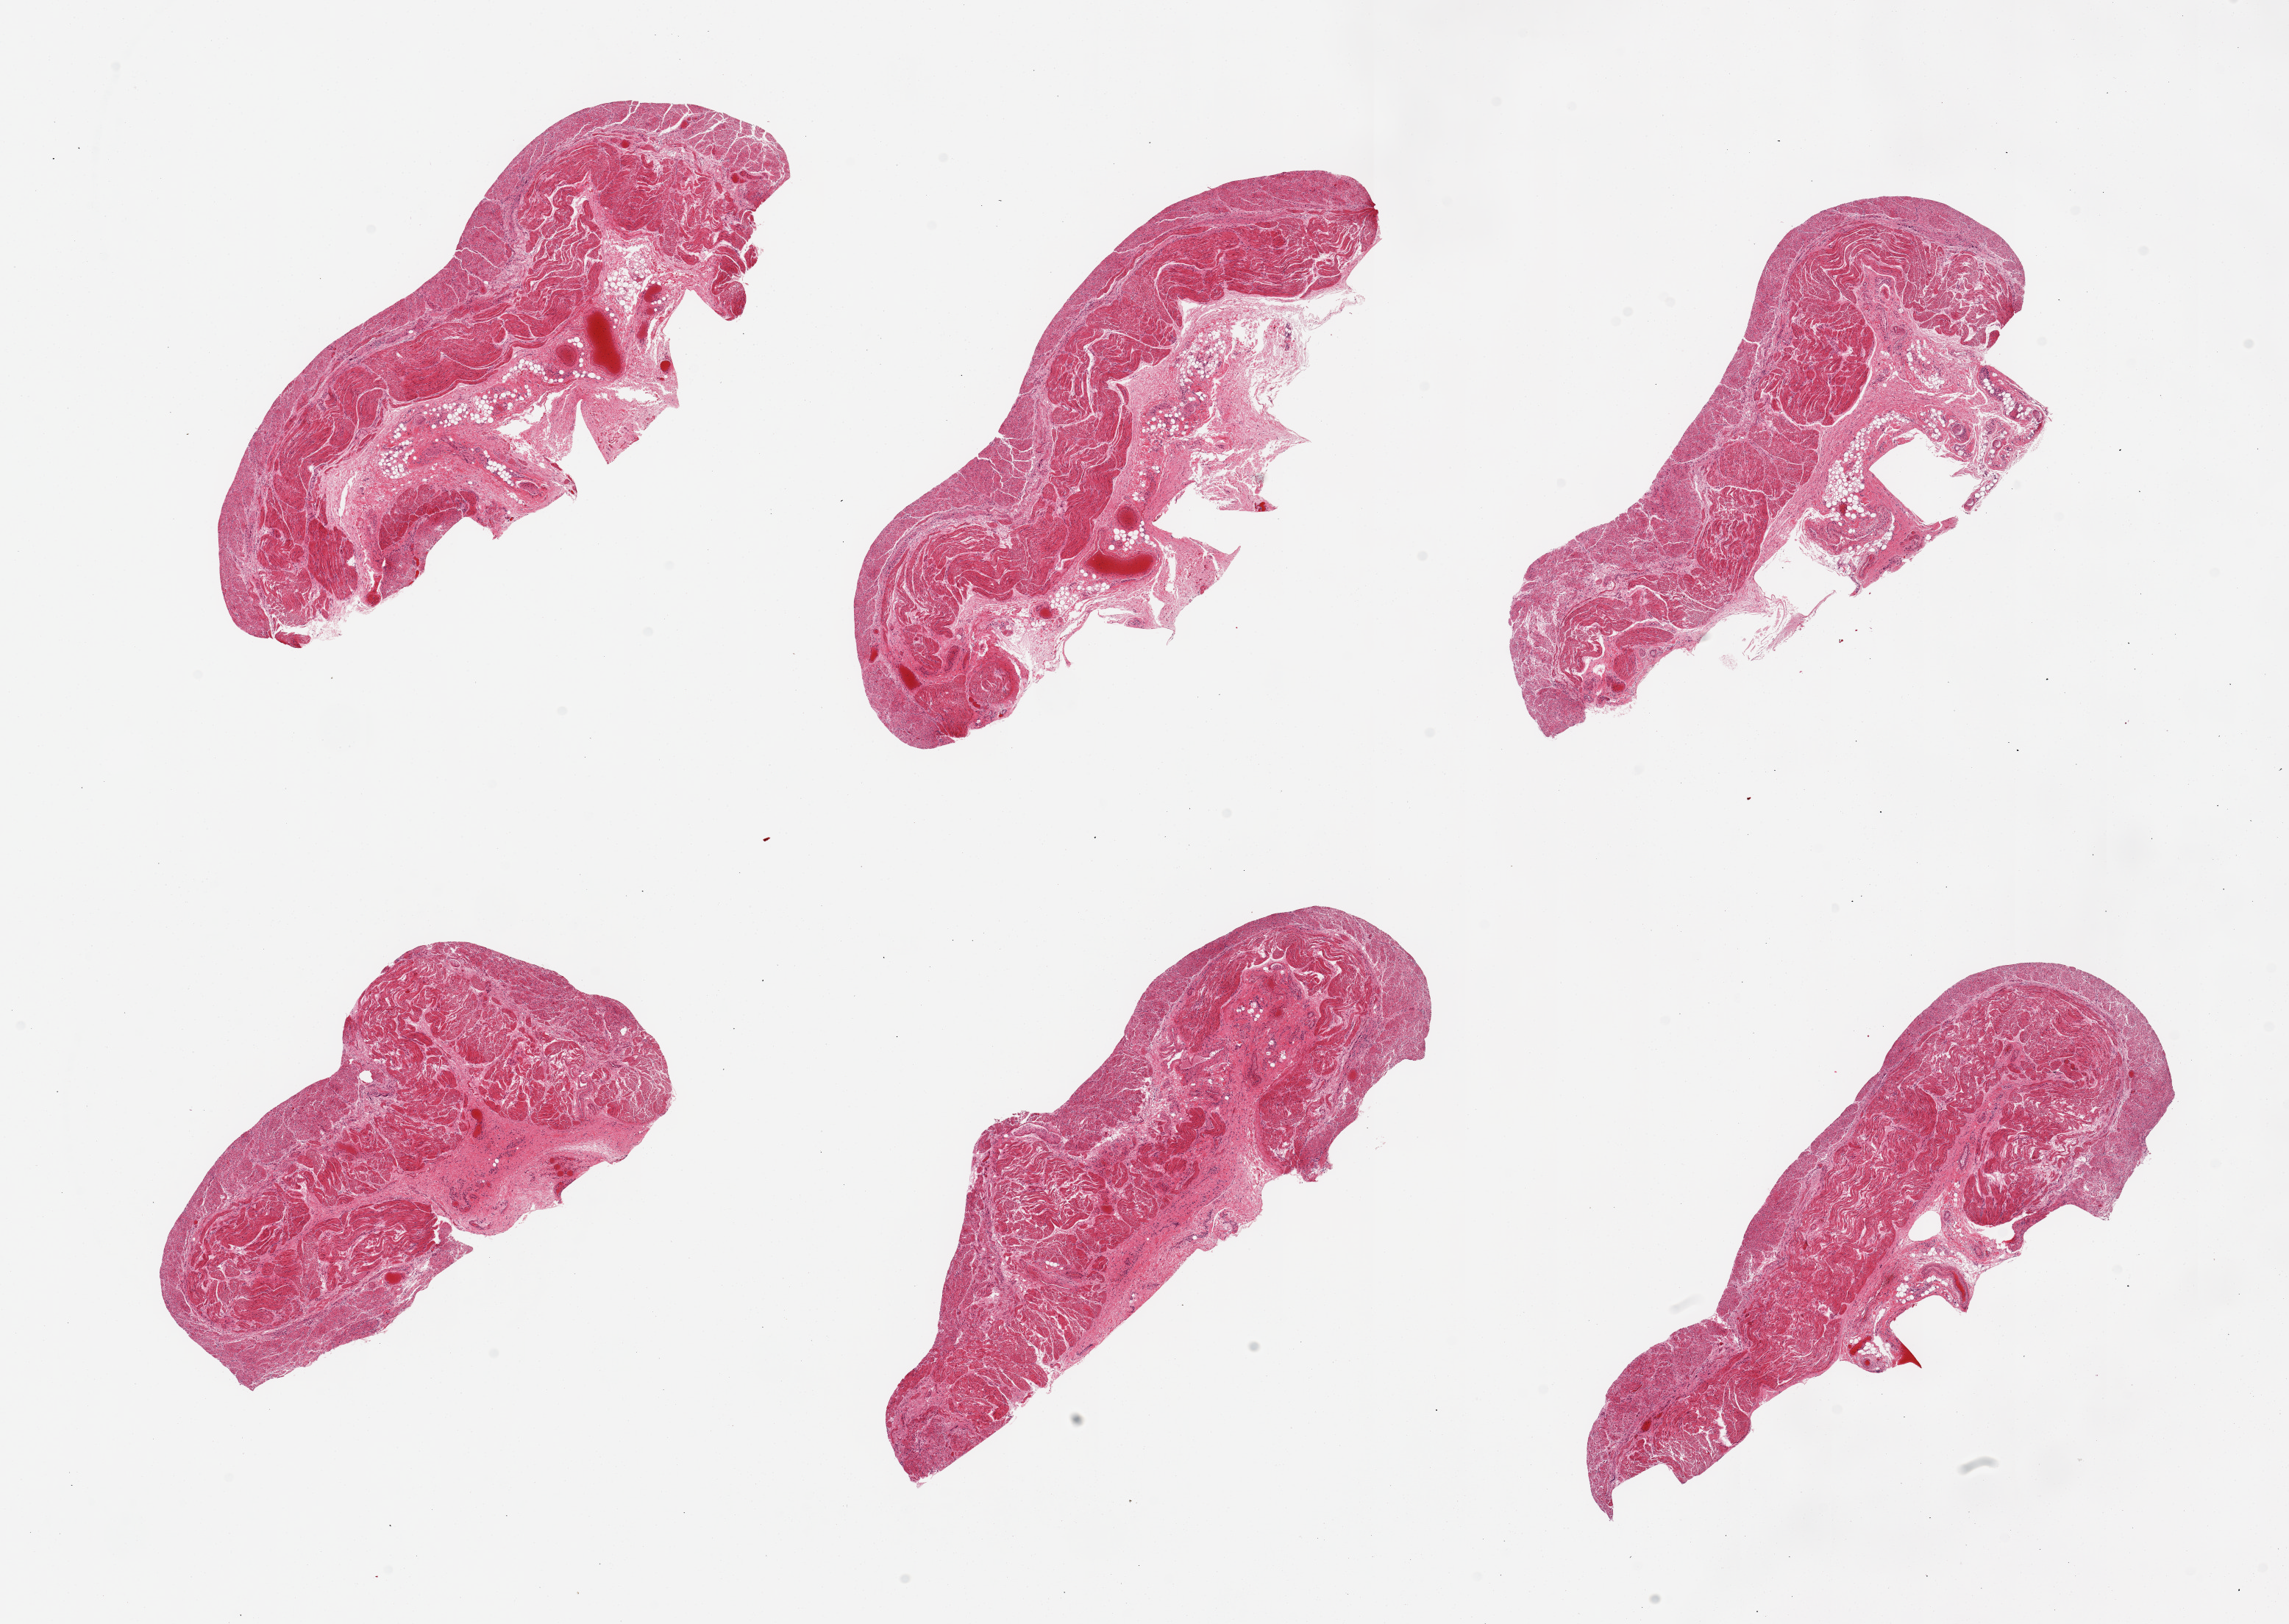
Hematoxylin and eosin (H&E) whole-slide image, brightfield — a low-resolution overview of the entire scanned area, about 24.6 x 17.5 mm (slide scanned at 20x). PAXgene-fixed, paraffin-embedded tissue. Target tissue: esophageal muscle. Donor tissue sample.
Pathologist's review note for this sample: 6 pieces, all muscularis, adherent serosa/fat up to~1.5mm.